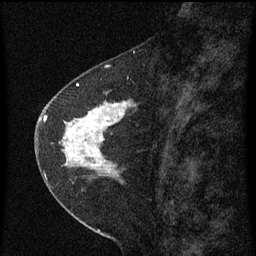
Breast MRI (dynamic contrast-enhanced), one sagittal slice. Dynamic contrast-enhanced series, image 2 of 3 at this slice position (ordered by acquisition). 1.5 T. TE 4.2 ms, TR 8 ms. 256 × 256 image matrix, field of view 180 × 180 mm. Patient: female, 47 years.
Annotated regions visible in this slice (semi-automatically segmented with operator editing):
- analysis volume of interest (the breast-tissue region the enhancement analysis was run in; not a lesion): bounding box <44,84,139,199> (left, top, right, bottom; pixels)
- tumour enhancement mask (voxels above the 70 % enhancement threshold inside the analysis volume of interest): <44,84,131,177>